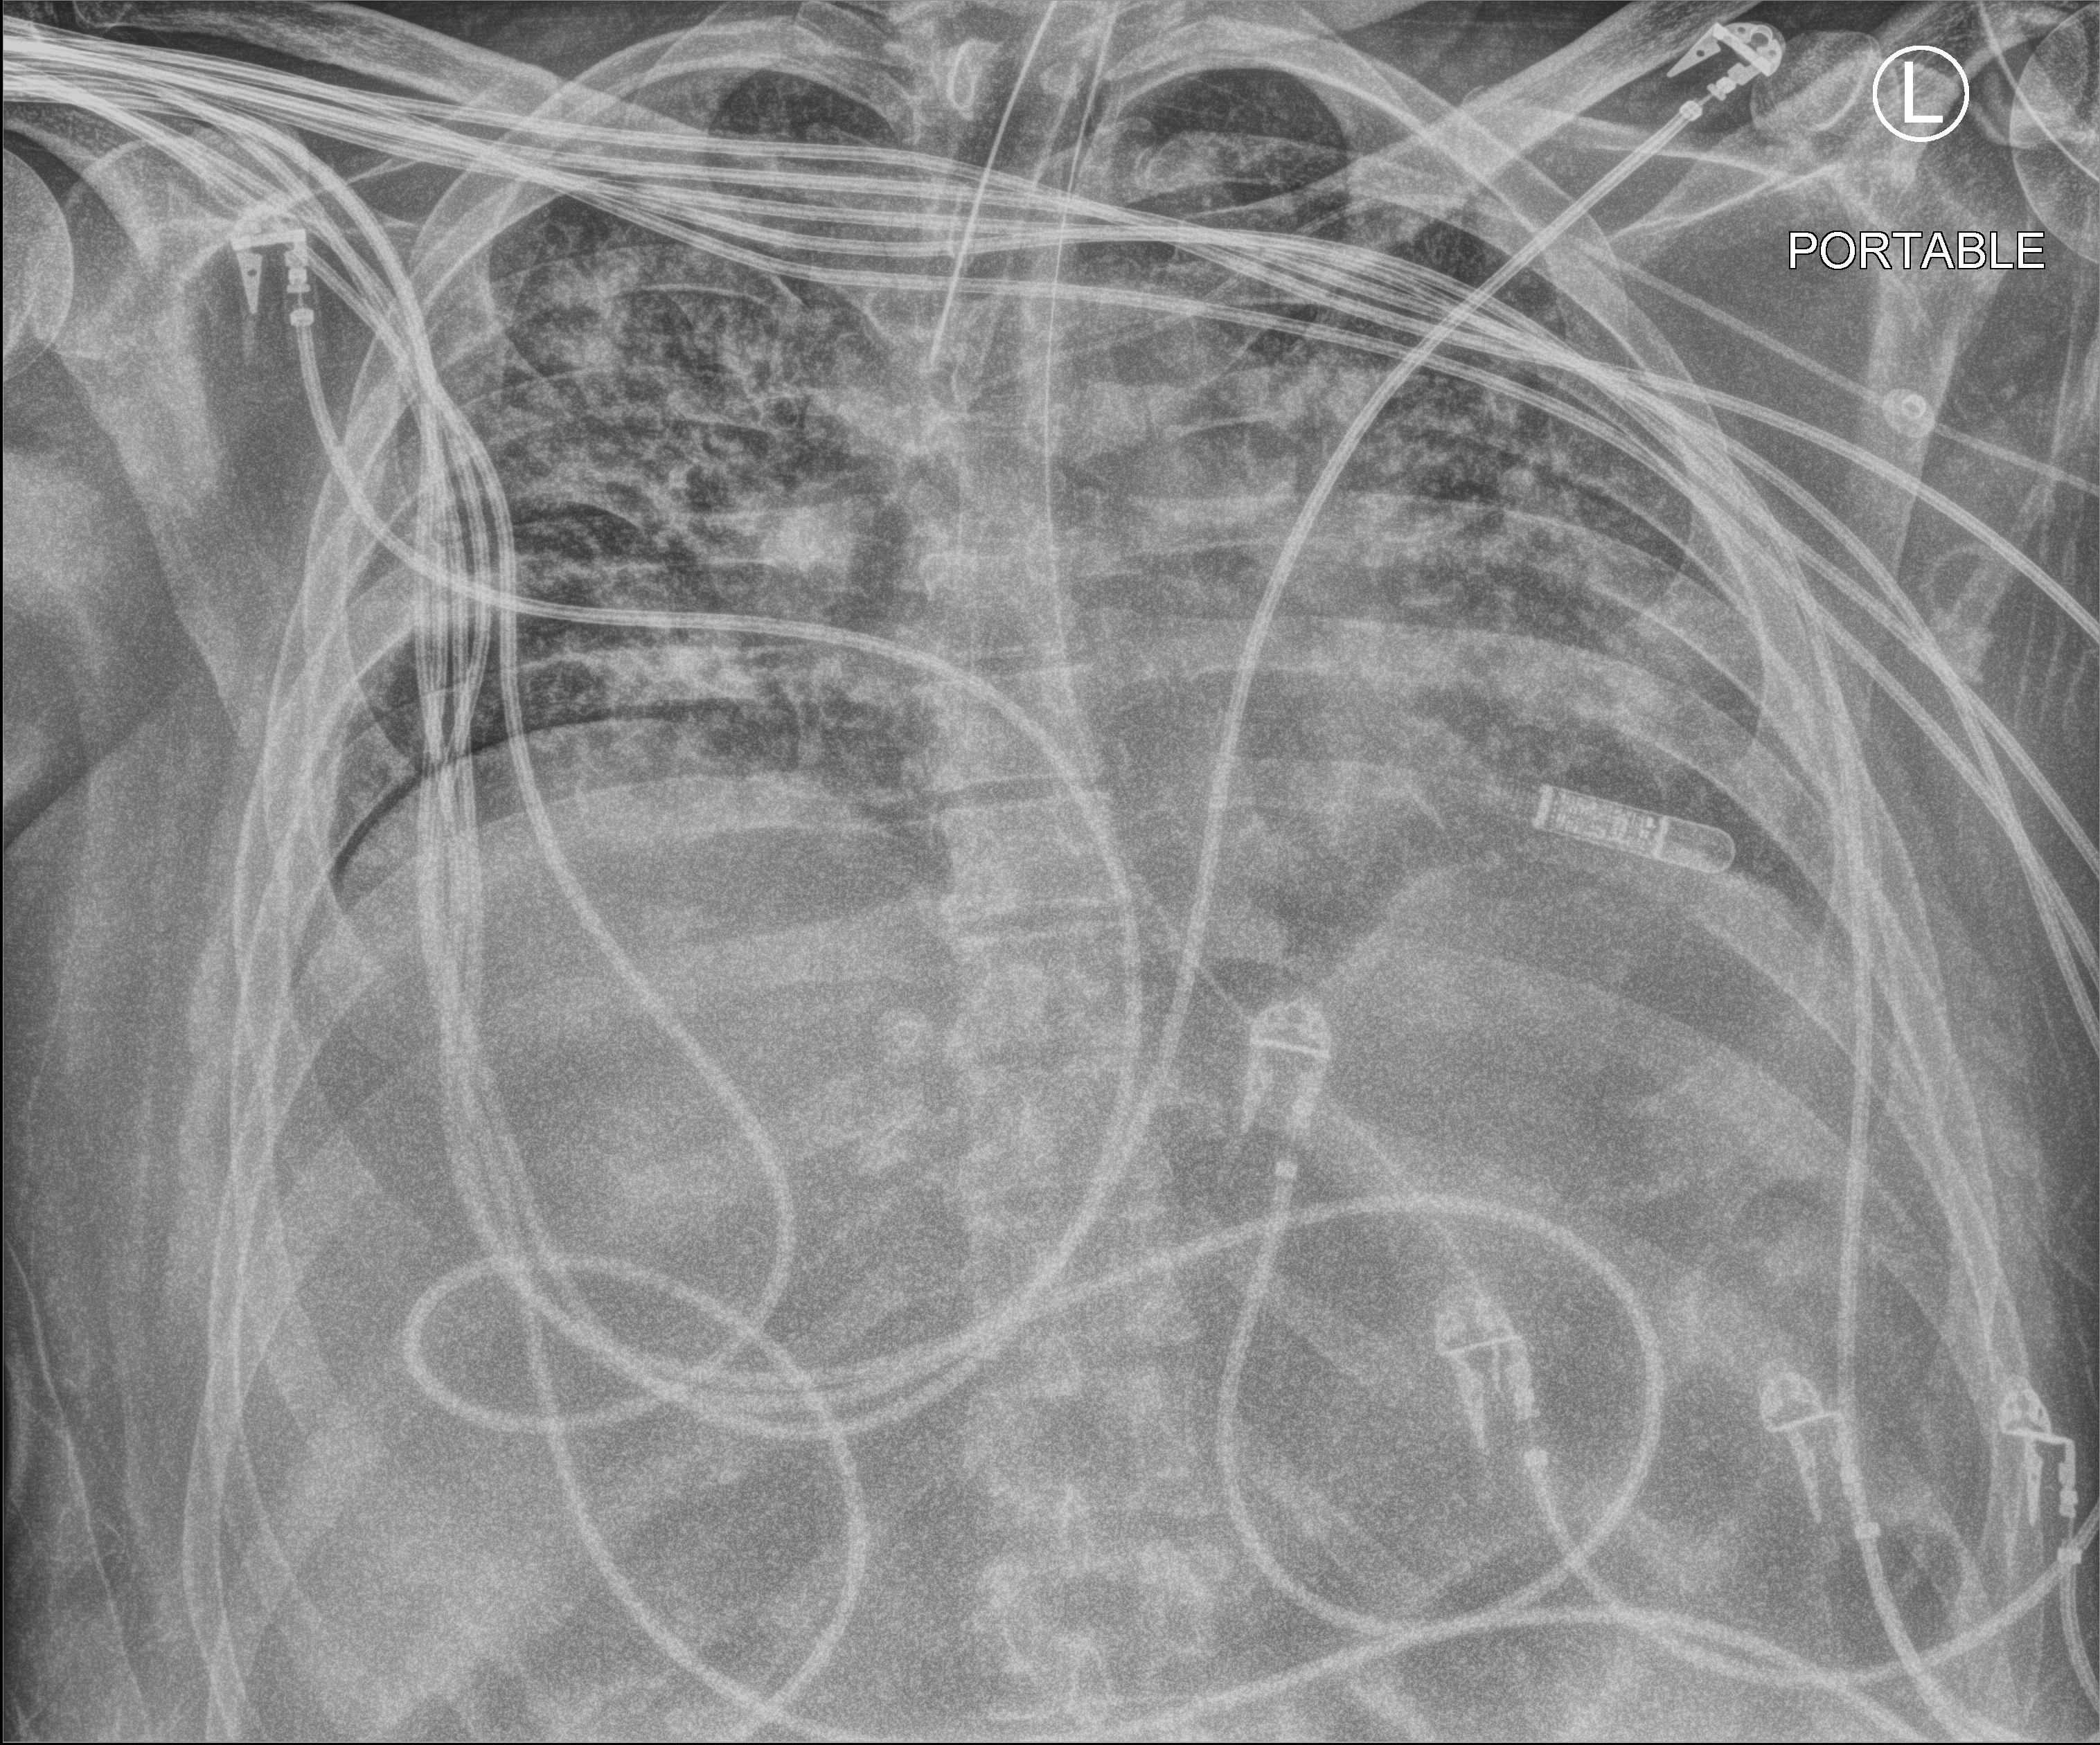
Bedside chest radiograph (computed radiography); anteroposterior (AP) projection. Male patient hospitalised with COVID-19, age 18–59 years.
Admission-level facts for this patient (not findings on this image; timing relative to this image not recorded):
- other chronic lung disease (admission record): yes